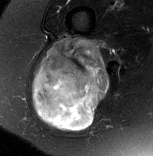
MRI of an extremity soft-tissue mass, one axial slice. T2-weighted fat-saturated. MR volume resampled by the dataset authors to the PET/CT grid (not the native acquisition matrix). 3.27 mm slice thickness. 153 × 156 image matrix, field of view 149 × 152 mm. Female patient. From the clinical record (not read from this slice): histological type: synovial sarcoma; grade: intermediate; site of the primary tumour: right buttock.
Structures marked on this image (expert contour drawn on MRI and transferred to this co-registered scan by the dataset authors):
- gross tumour volume including surrounding oedema: box from (x=33, y=36) to (x=109, y=132) px
- gross tumour volume (mass): (x=33, y=36)–(x=109, y=132)